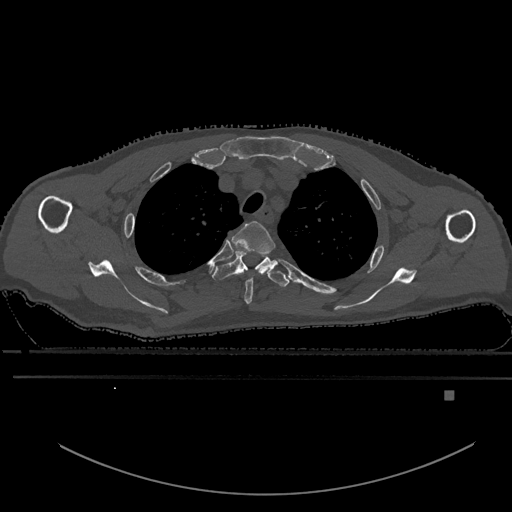
CT including the spine, one axial slice; position 470 of 969 along the scan axis; bone window (W 1800 / L 400 HU); 0.5 mm slice thickness; 512 × 512 image matrix. Male patient, age 82 years. Case-level facts recorded for this patient, not image findings: primary cancer: prostate.
Structures marked on this image (semi-automatic segmentation, software-assisted and operator-edited):
- T2 vertebra: box from (x=232, y=221) to (x=275, y=305) px
- T3 vertebra: (x=212, y=251)–(x=289, y=287)